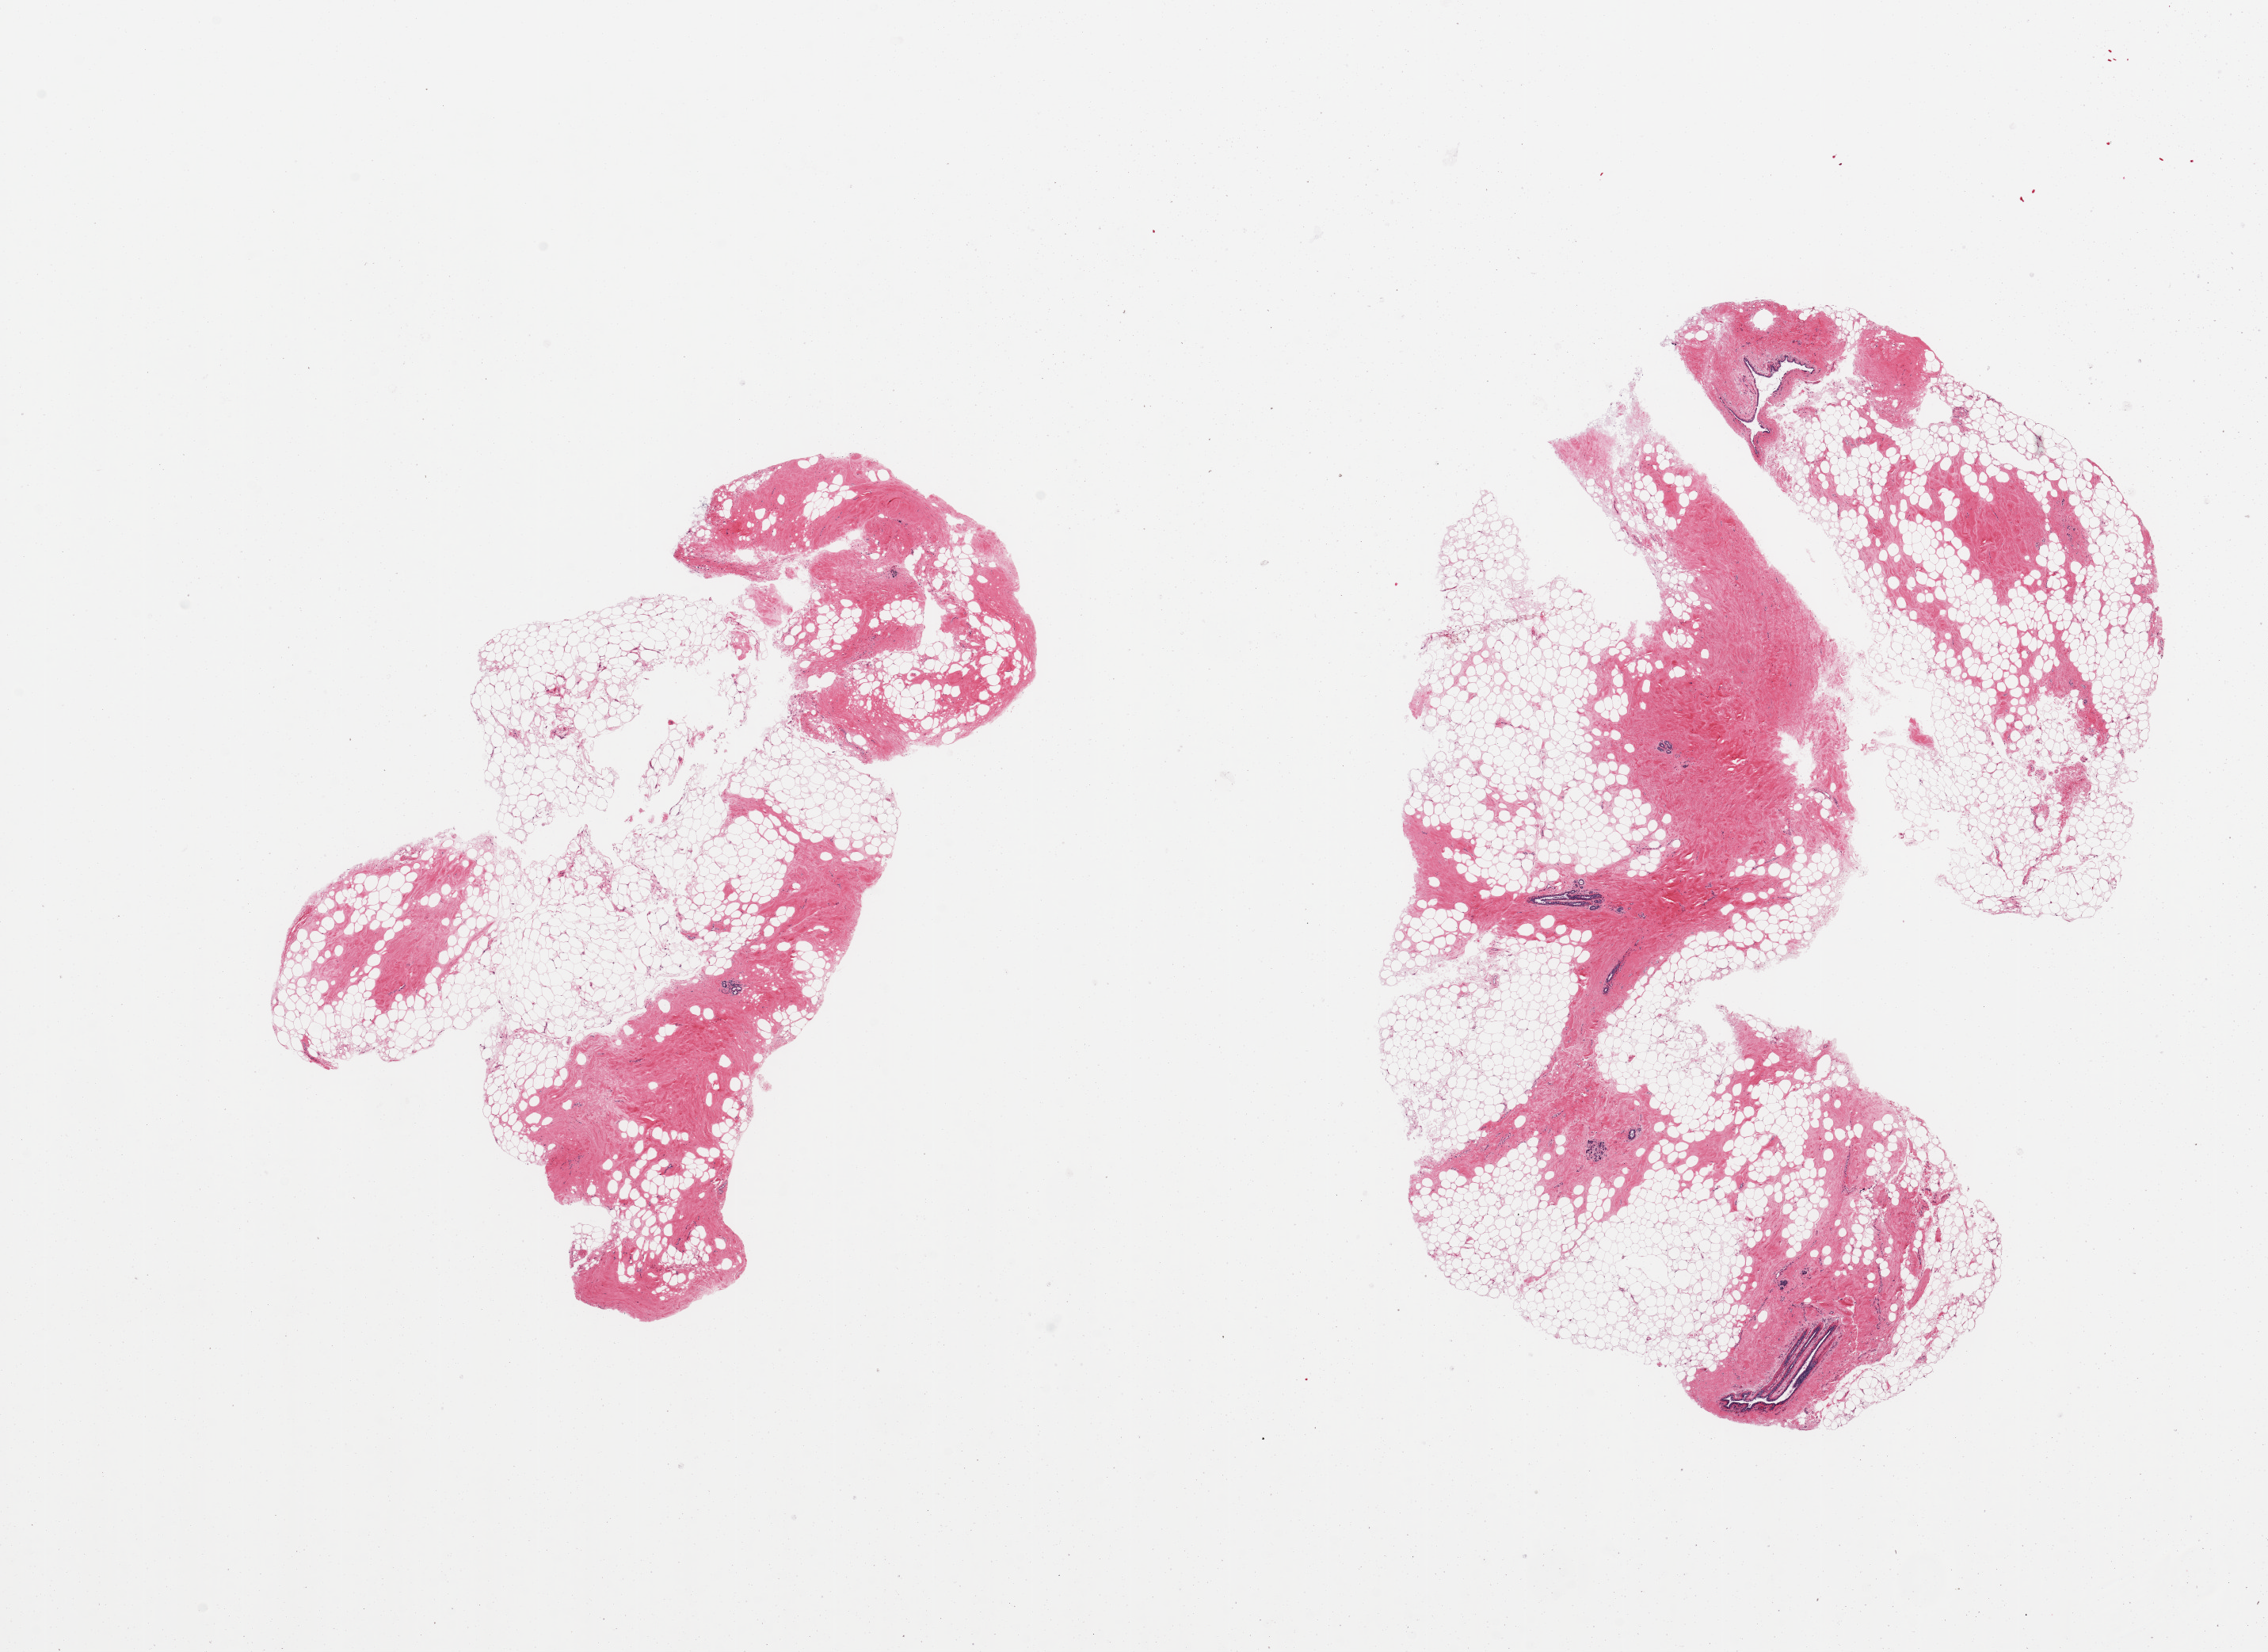
Whole-slide image, hematoxylin and eosin (H&E) stain — whole scanned area (about 22.6 x 16.5 mm, acquisition: 20x scan) shown as a low-resolution overview; PAXgene-fixed paraffin-embedded (PFPE) section; section of breast (target tissue); tissue donor sample. Donor: female.
Pathologist's review note for this sample: 2 pieces, mainly fibroadipose elements; trace atrphic duct/lobular units.